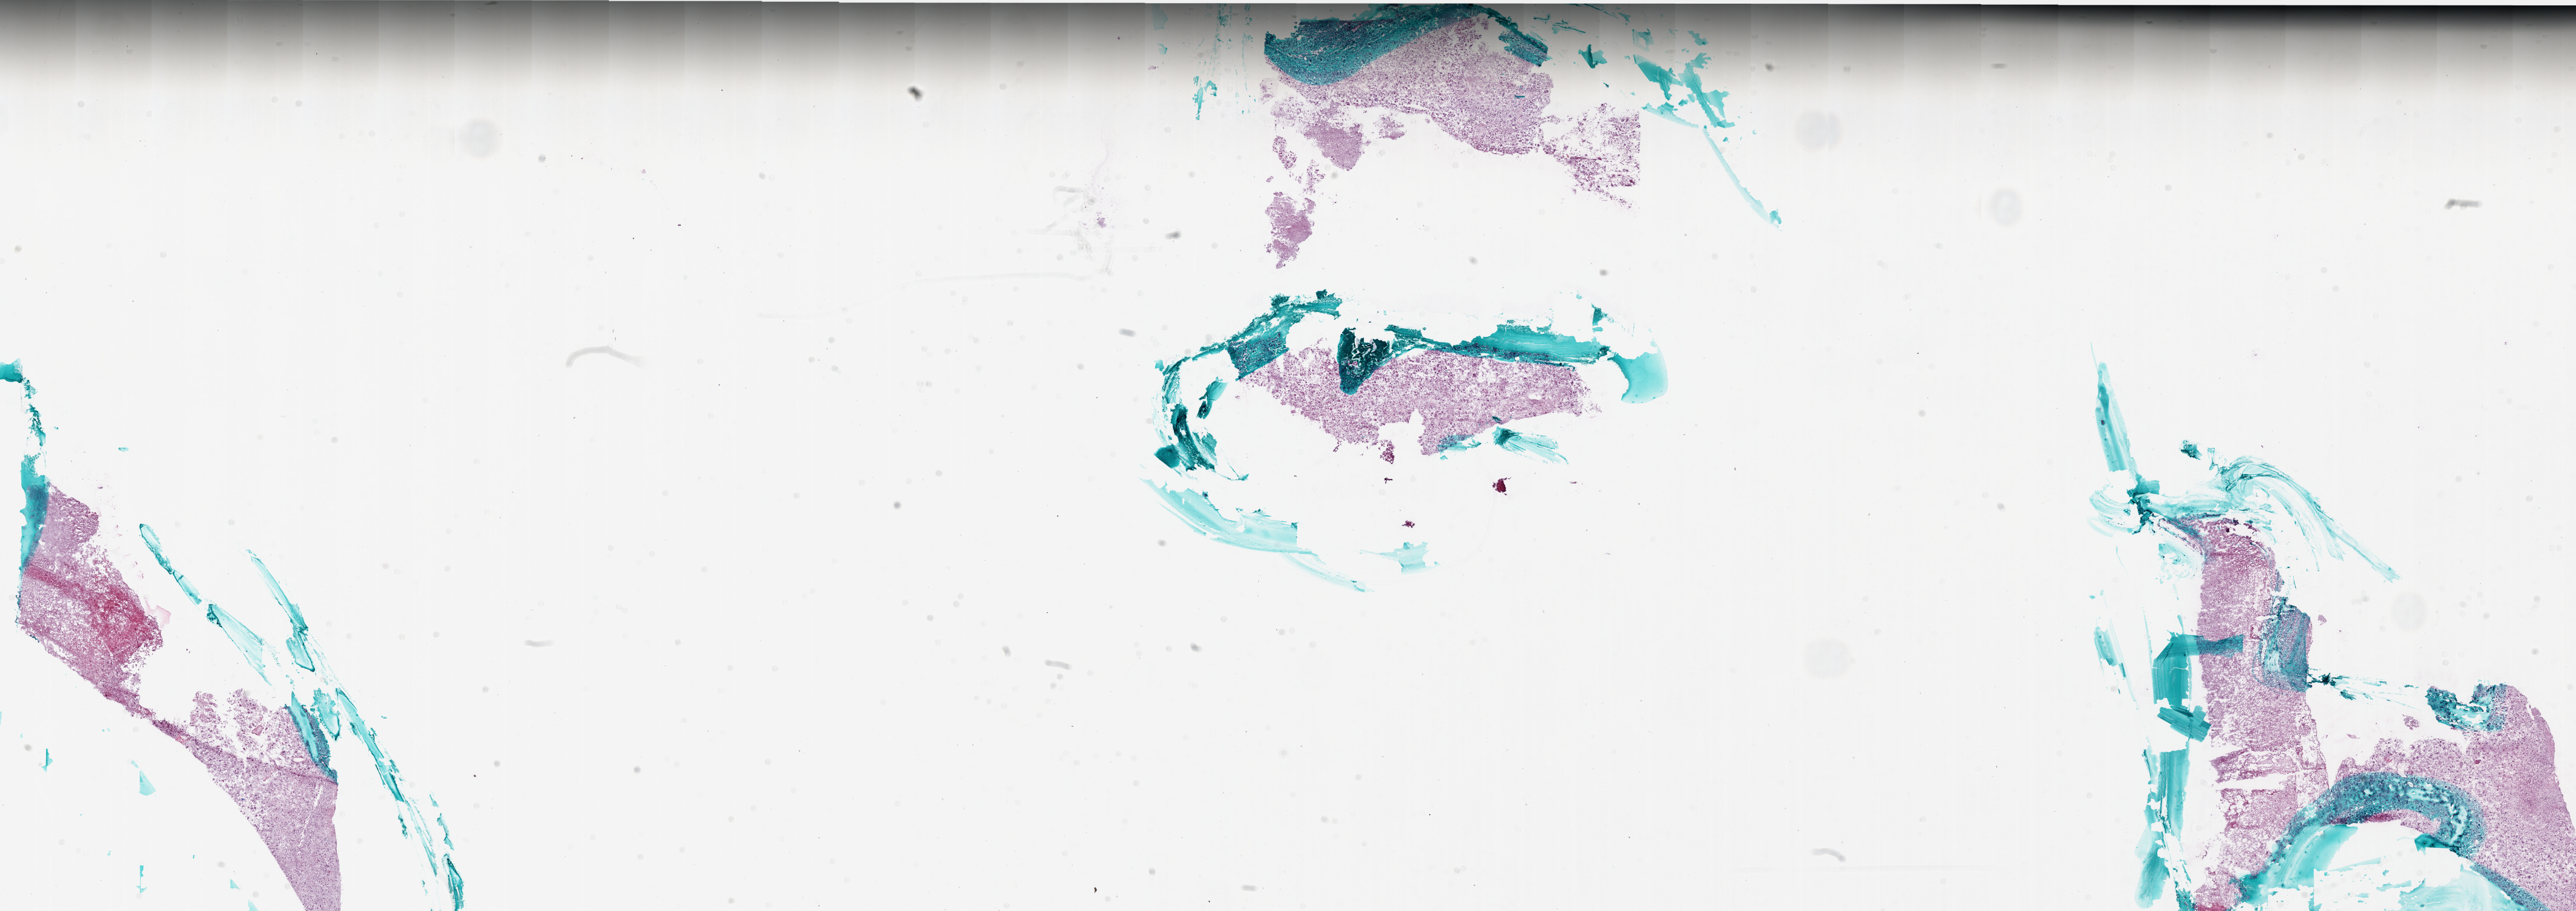
Whole-slide histology image, Hematoxylin and eosin (H&E) stained, whole scanned area (about 34.0 x 12.0 mm, slide scanned at 20x) shown as a low-resolution overview, frozen section from the bottom of the tissue portion, sample: primary tumour, brain. Male, age 57 years at initial diagnosis. Pathologist review of this section (percent, as recorded): tumour cells 75%, tumour nuclei 95%, normal cells 0%, stromal cells 25%, necrosis 0%.
* diagnosis: Glioblastoma